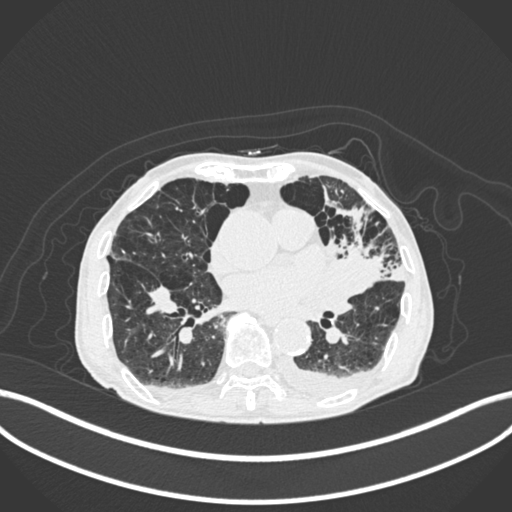
Chest CT, one axial slice. Position 93 of 400 along the scan axis. 120 kVp. Lung window (W 1500 / L -600 HU). 512 × 512 image matrix, field of view 400 × 400 mm. Male patient, age 90 years or older. From the clinical record (not read from this slice): clinical TNM (as recorded): T2b N1 M0.
Structures marked on this image (rectangle marked by the reading radiologist):
- lung tumour (recorded histology: squamous cell carcinoma): bounding box (x1, y1, x2, y2) in pixels: (323, 232, 387, 305)